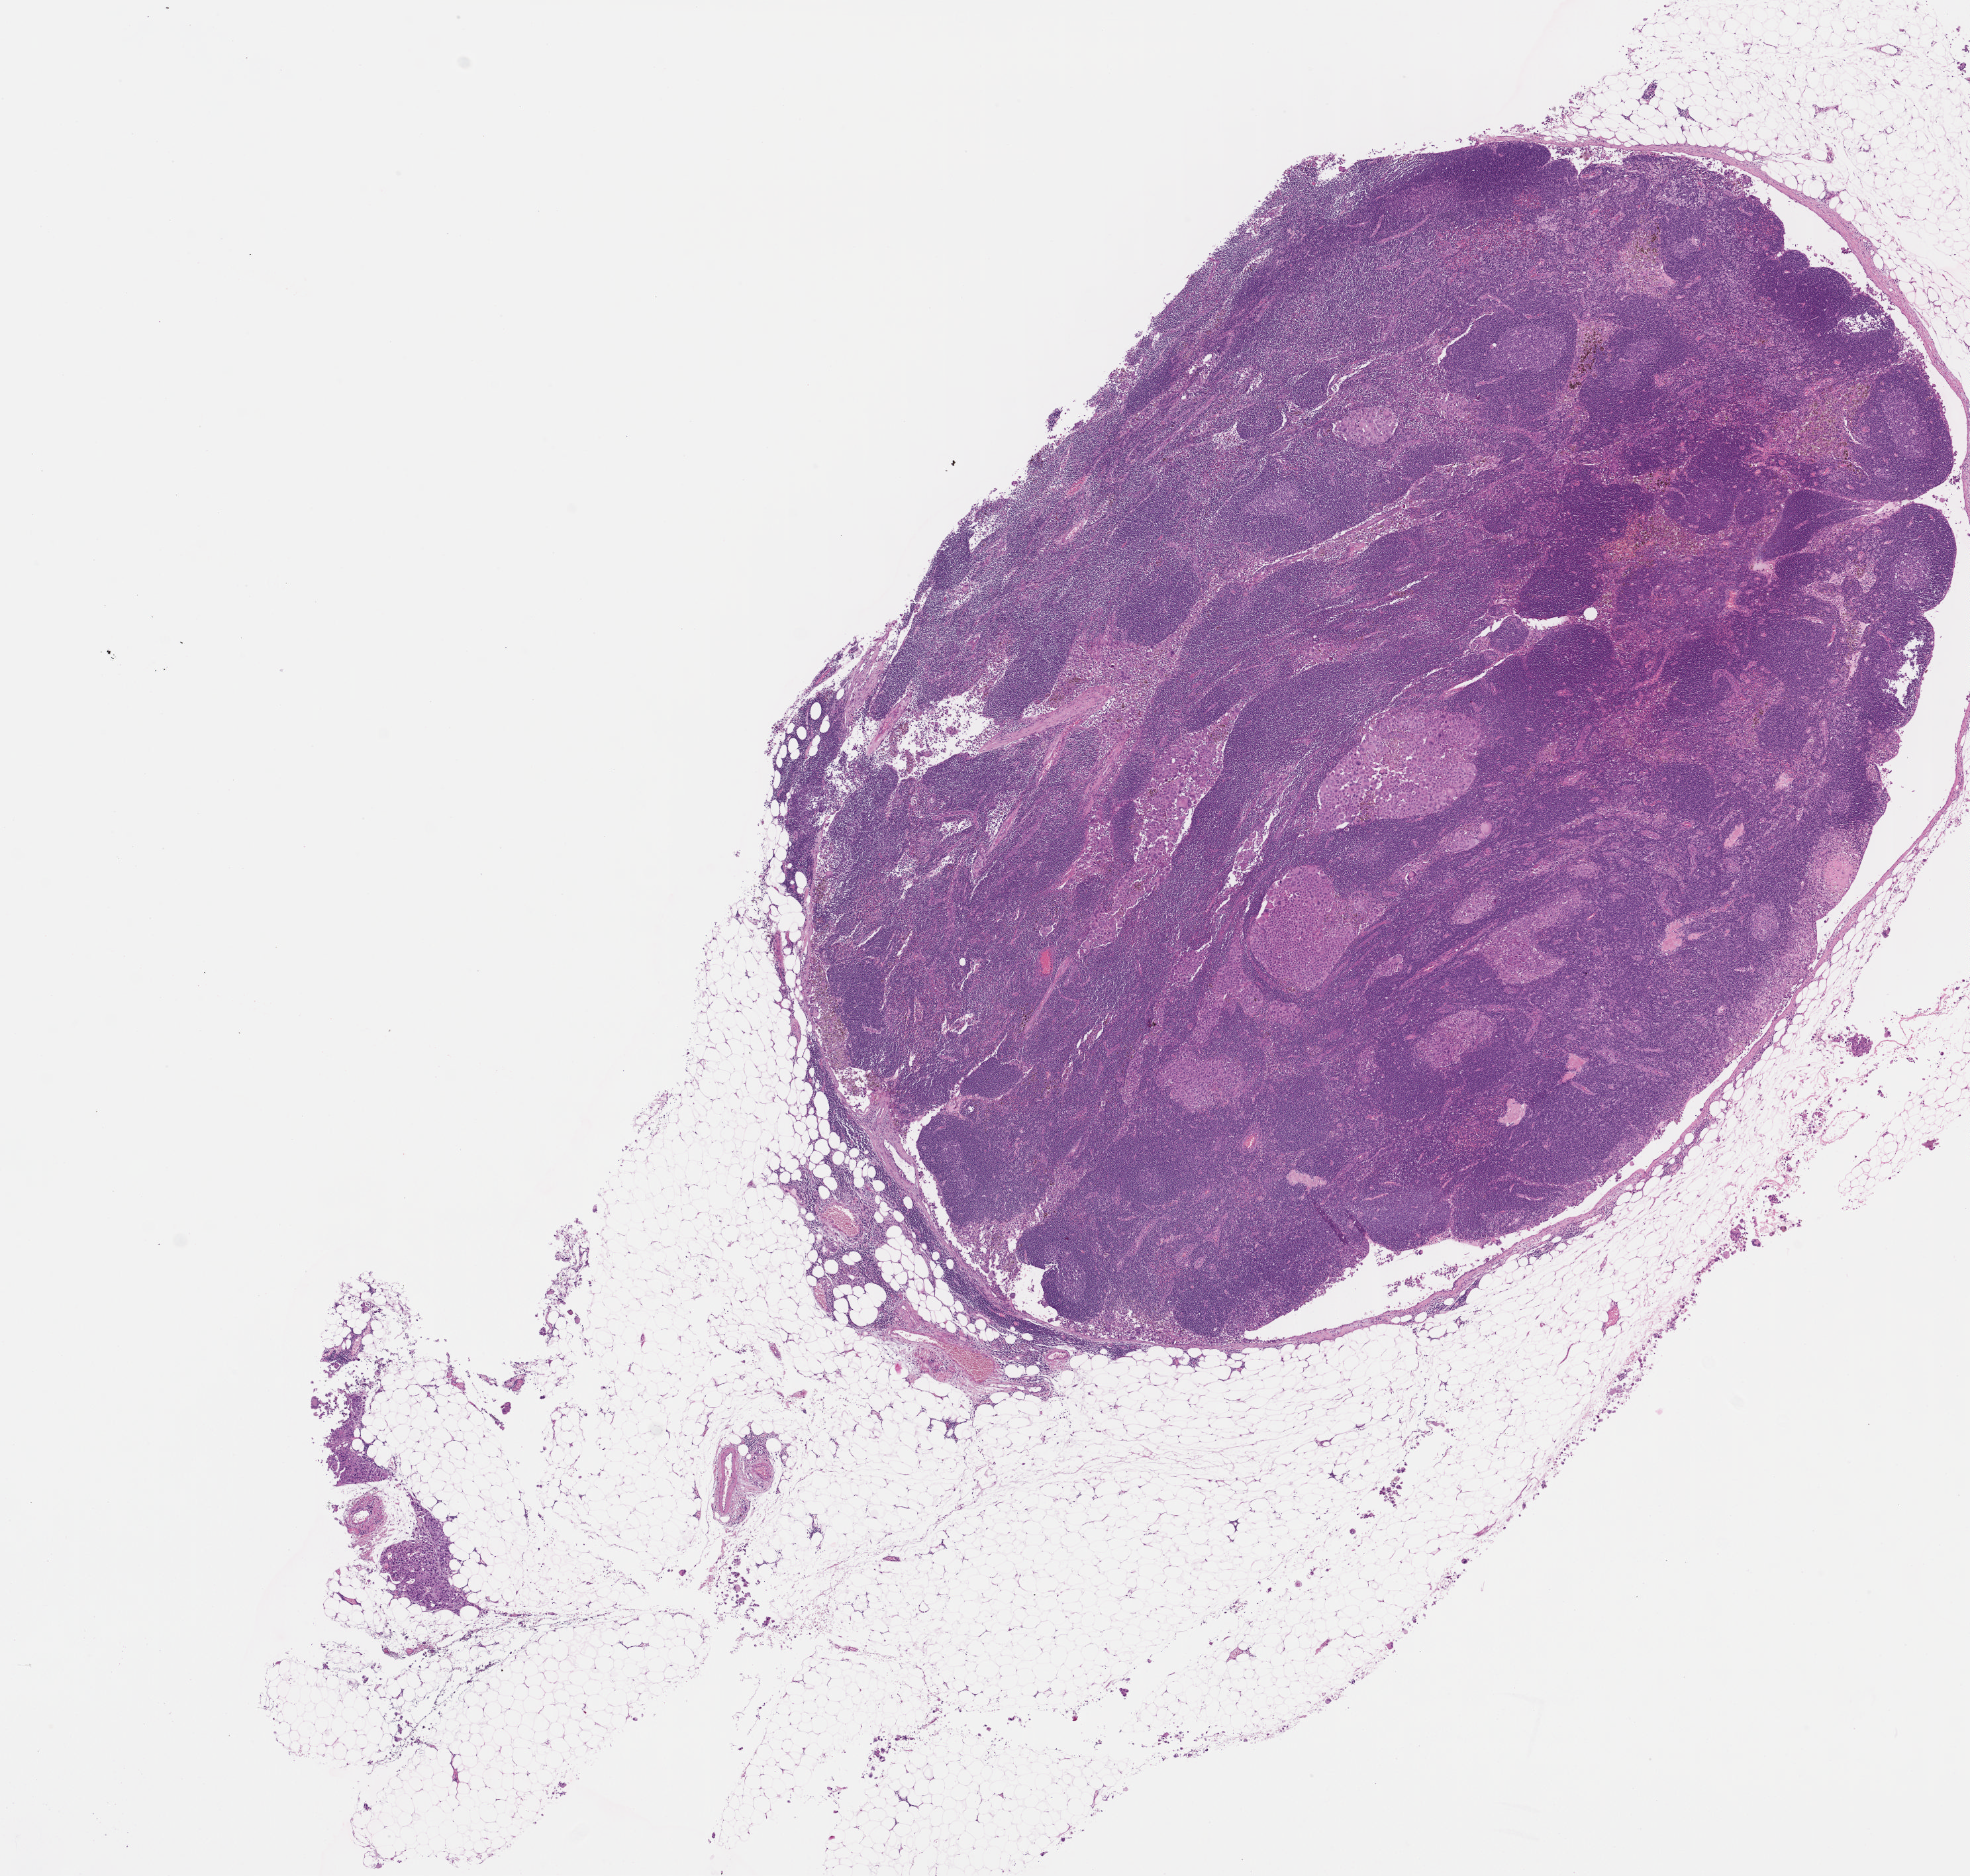
Digitized Hematoxylin and eosin (H&E) stained tissue section (whole slide) — whole scanned area (about 11.7 x 11.1 mm, slide scanned at 40x) shown as a low-resolution overview, FFPE section, primary tumour sample from the skin. Patient: male, age at initial diagnosis 66 years.
Pathologic diagnosis: Malignant melanoma, NOS.